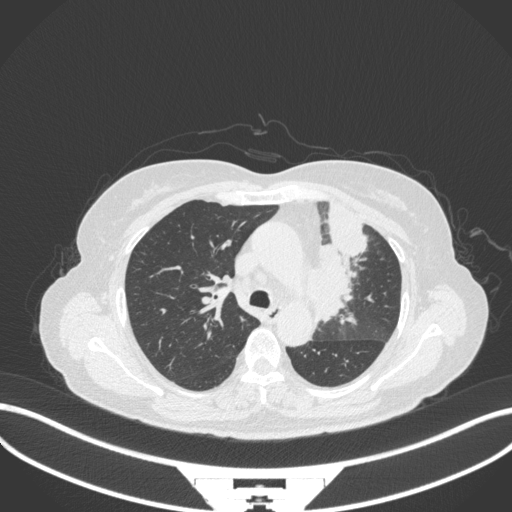
Chest CT, one axial slice; position 228 of 382 along the scan axis; lung window (W 1500 / L -600 HU); 512 × 512 image matrix, field of view 400 × 400 mm. Female patient, age 64 years. Case-level facts recorded for this patient, not image findings: clinical TNM (as recorded): T2a N2 M0.
Annotated regions visible in this slice (bounding box drawn by a radiologist):
- lung tumour (recorded histology: adenocarcinoma): bounding box (x1, y1, x2, y2) in pixels: (306, 196, 375, 323)